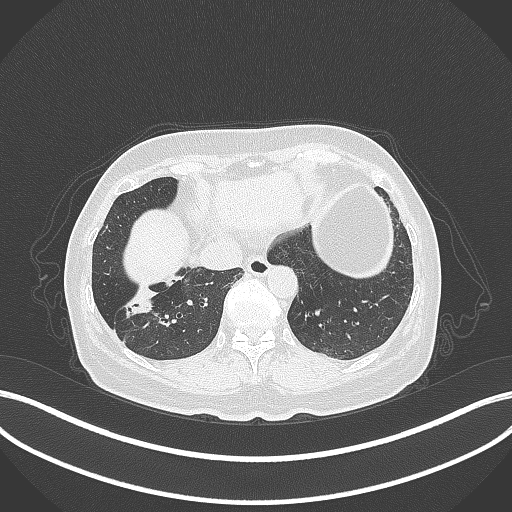
Chest CT, one axial slice; position 100 of 429 along the scan axis; reconstruction kernel B70f; lung window (W 1500 / L -600 HU); 512 × 512 image matrix. Female patient, age 67 years. From the clinical record (not read from this slice): clinical TNM (as recorded): T1c N1 M0; histopathological grade: G2-3.
Outlined on this slice (rectangle marked by the reading radiologist):
- lung tumour (recorded histology: adenocarcinoma): box from (x=116, y=283) to (x=165, y=327) px